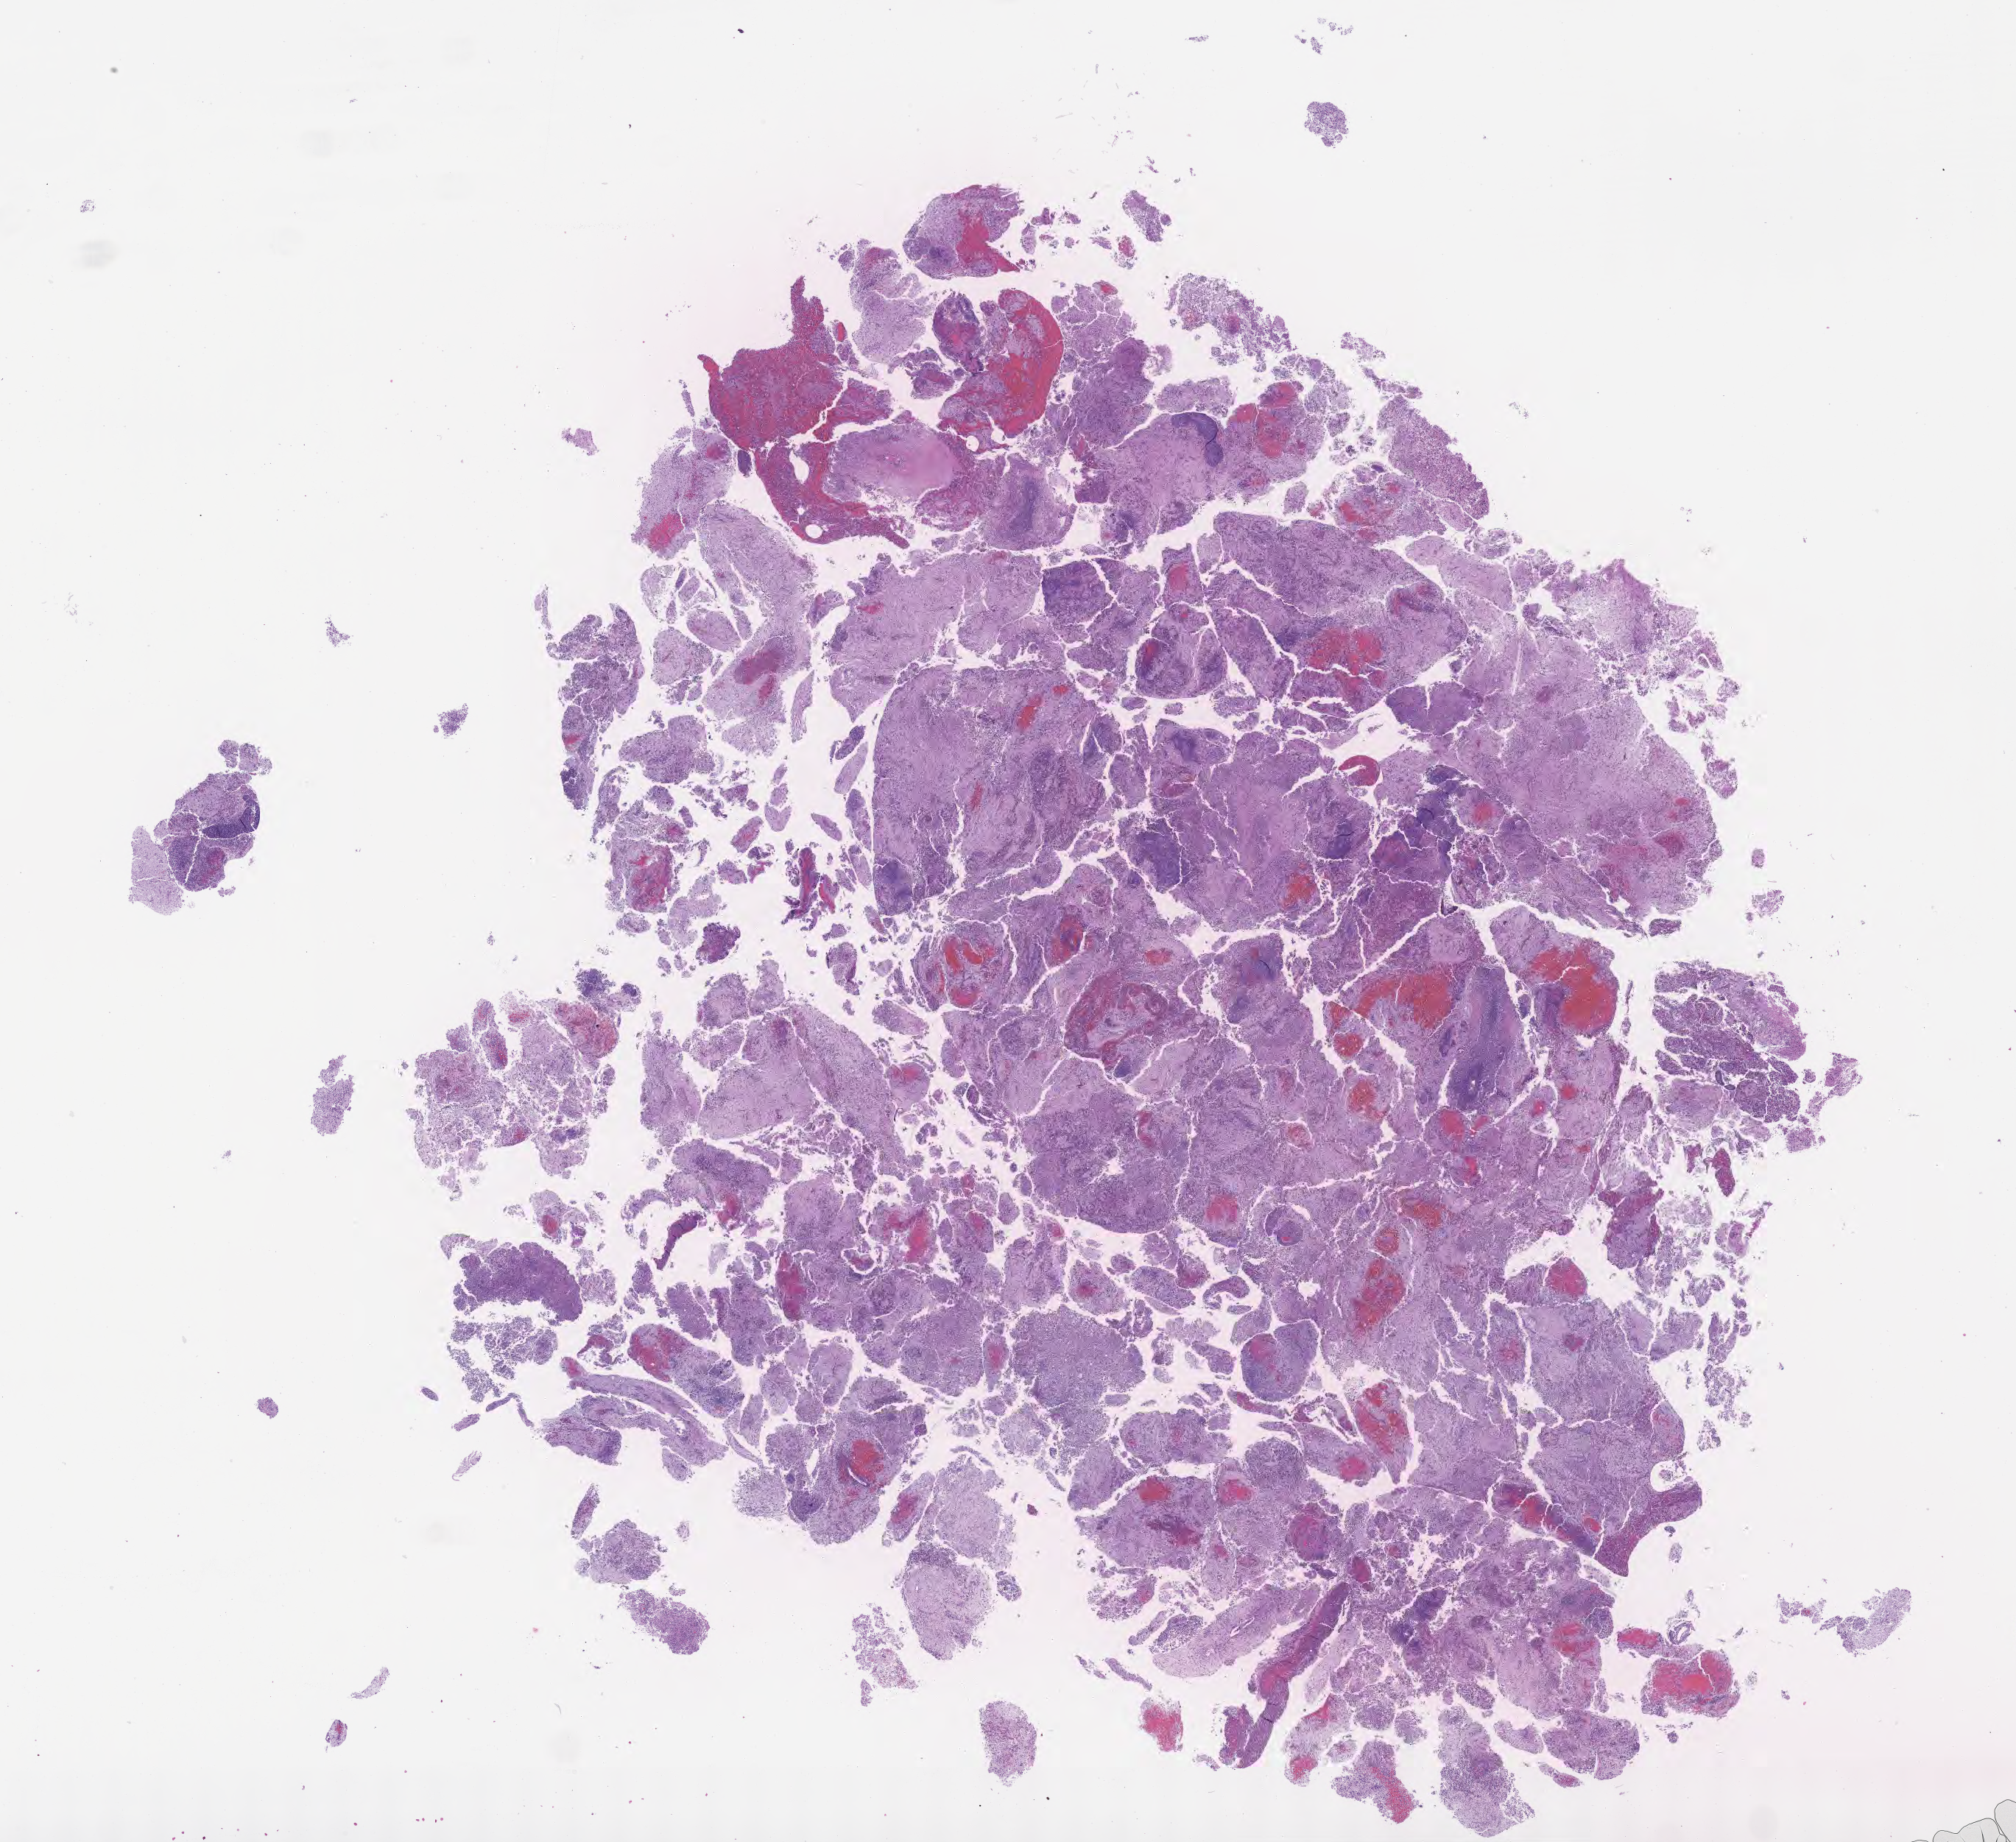
Digitized H&E-stained section — a low-resolution overview of the entire scanned area, about 22.1 x 20.2 mm. Specimen: tumor tissue. Site: brain. Patient male; aged 51.
* diagnosis: Diffuse large B-cell lymphoma, NOS